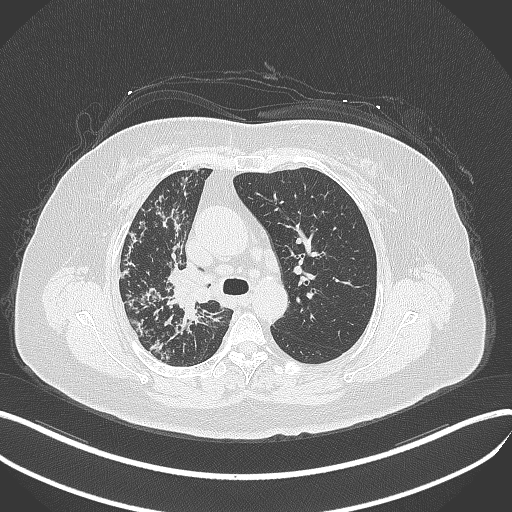
Chest CT, one axial slice. Slice 244 of 376 in the series (ordered by position). 120 kVp. Lung window (W 1500 / L -600 HU). 512 × 512 image matrix, field of view 400 × 400 mm. Patient: female, 60 years. From the clinical record (not read from this slice): clinical TNM (as recorded): T1c N0 M0; histopathological grade: G1-G2.
Structures marked on this image (bounding box drawn by a radiologist):
- lung tumour (recorded histology: squamous cell carcinoma): bounding box (x1, y1, x2, y2) in pixels: (171, 268, 211, 312)